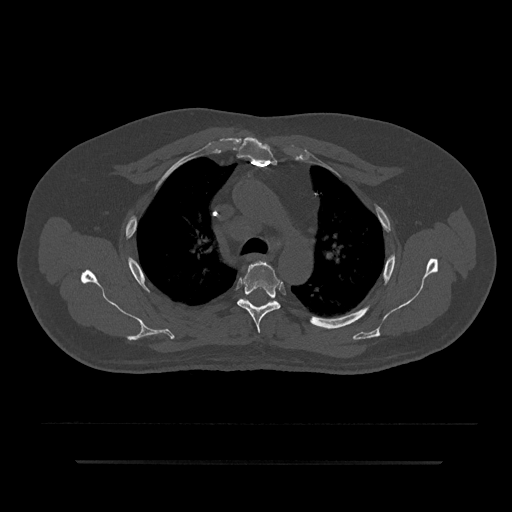
CT including the spine, one axial slice. Position 614 of 797 along the scan axis. Reconstruction kernel Br40s/3. 120 kVp. Bone window (W 1800 / L 400 HU). 512 × 512 image matrix, field of view 464 × 464 mm. Patient: male, 59 years. From the clinical record (not read from this slice): primary cancer: bile ducts.
Structures marked on this image (semi-automatically segmented with operator editing):
- T4 vertebra: bounding box (x1, y1, x2, y2) in pixels: (237, 261, 283, 333)
- T5 vertebra: (237, 298, 278, 304)